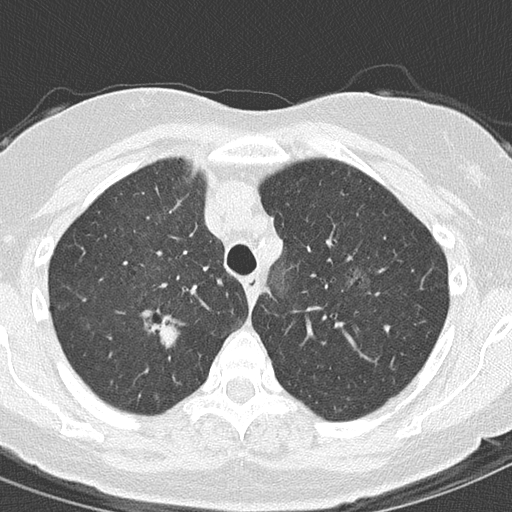
Chest CT (low-dose screening protocol), one axial image. Second annual screen. Lung window (W 1500 / L -600 HU). Slice 40 of 157 in the series. Female, age 61 years at enrolment. Current smoker at enrolment.
Expert-annotated lung lesion, bounding box (x1, y1, x2, y2) in pixels: (146, 307, 188, 345). Reader record for this screening exam (exam-level; its link to the box is not recorded): non-calcified nodule or mass ≥4 mm, right upper lobe, 15 × 10 mm, spiculated (stellate) margins, ground glass attenuation, pre-existing on the prior screen: yes; interval growth: yes. Lung cancer was diagnosed 91 days after this screen: adenocarcinoma, NOS, right upper lobe, moderately differentiated (G2), stage IA (AJCC 6th edition), 20 mm at pathology.